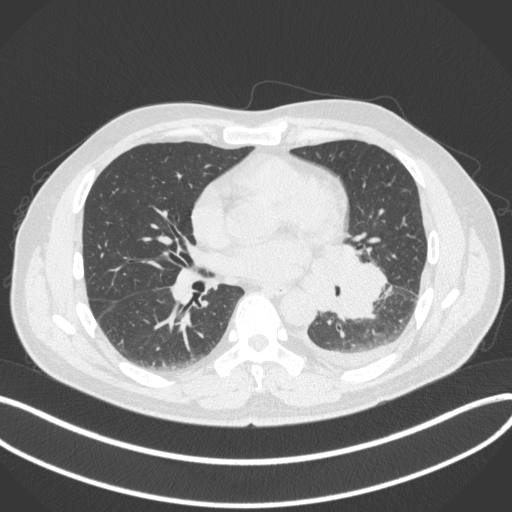
Chest CT, one axial slice. Slice 173 of 350 in the series (ordered by position). Reconstruction kernel B31f. Lung window (W 1500 / L -600 HU). 1 mm slice thickness. 512 × 512 image matrix, field of view 400 × 400 mm. Patient: male, 58 years. Case-level facts recorded for this patient, not image findings: clinical TNM (as recorded): T3 N1 M1b; histopathological grade: G3.
Structures marked on this image (bounding box drawn by a radiologist):
- lung tumour (recorded histology: small cell carcinoma): box from (x=308, y=233) to (x=391, y=324) px